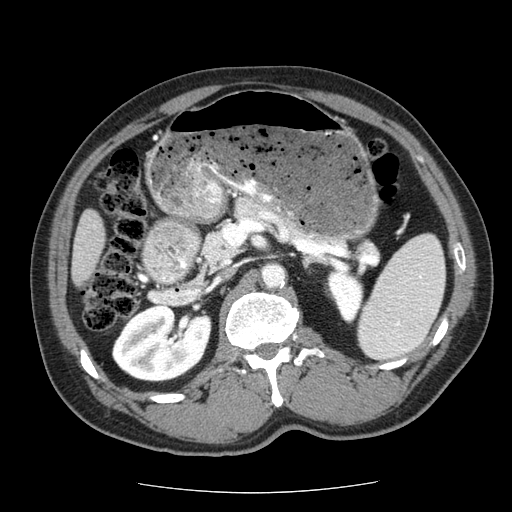
Contrast-enhanced abdominal CT (liver protocol), one axial slice. Position 15 of 85 along the scan axis. Soft-tissue window (W 400 / L 40 HU). 512 × 512 image matrix. Case-level facts recorded for this patient, not image findings: diagnosis: hepatocellular carcinoma (patient treated with transarterial chemoembolisation; whether this scan precedes or follows treatment is not stated here); TNM stage (as recorded): Stage-IIIA; Child-Pugh class: A; tumour nodularity: multinodular; tumour size: 8 cm.
Structures marked on this image (semi-automatically segmented with operator editing):
- liver parenchyma outside the tumour (the mass and vessels are separate outlines, so this box may not span the whole liver): bounding box [x1, y1, x2, y2] px = [72, 210, 106, 286]